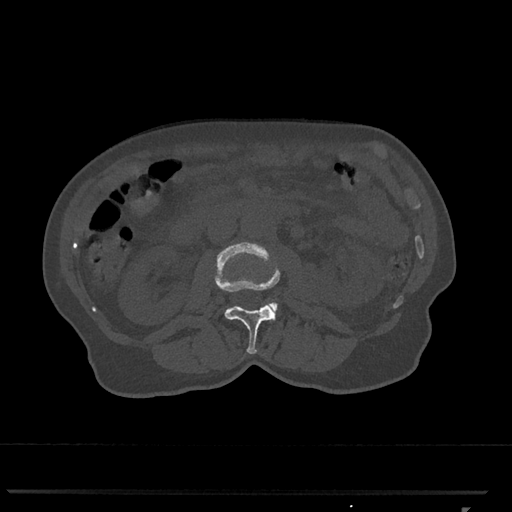
CT including the spine, one axial slice; slice 319 of 793 in the series (ordered by position); reconstruction kernel Br40s/3; 120 kVp; bone window (W 1800 / L 400 HU); 512 × 512 image matrix, field of view 380 × 380 mm. Patient: female, 62 years. From the clinical record (not read from this slice): primary cancer: renal.
Outlined on this slice (semi-automatic segmentation, software-assisted and operator-edited):
- L2 vertebra: bounding box [x1, y1, x2, y2] px = [214, 242, 281, 354]
- L3 vertebra: [268, 302, 278, 310]